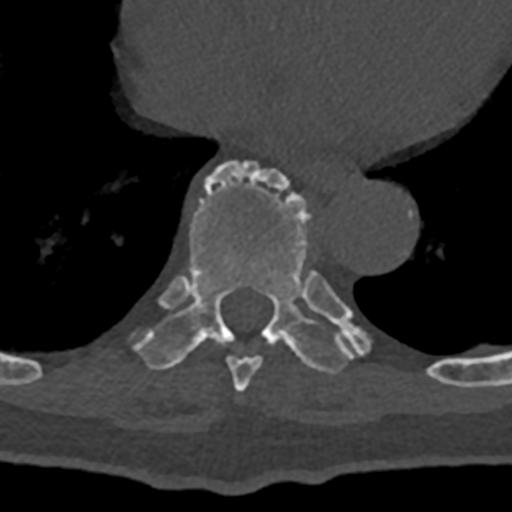
CT including the spine, one axial slice. Slice 673 of 797 in the series (ordered by position). Reconstruction kernel Br40s/3. 120 kVp. Bone window (W 1800 / L 400 HU). 0.5 mm slice thickness. 512 × 512 image matrix, field of view 160 × 160 mm. Male patient, age 74 years. From the clinical record (not read from this slice): primary cancer: renal.
Structures marked on this image (semi-automatically segmented with operator editing):
- T8 vertebra: bounding box (x1, y1, x2, y2) in pixels: (227, 356, 262, 393)
- T9 vertebra: (132, 162, 432, 375)